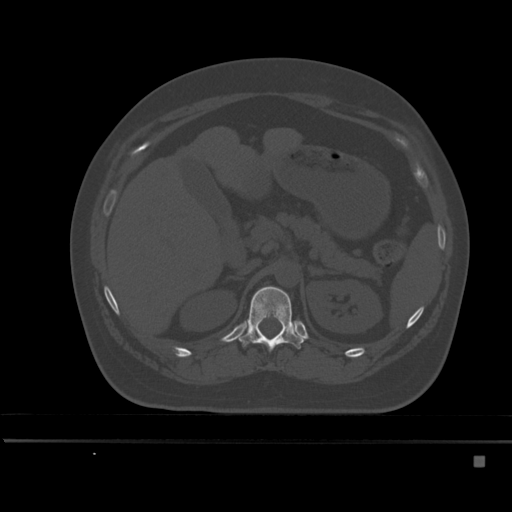
CT including the spine, one axial slice. Position 214 of 495 along the scan axis. Bone window (W 1800 / L 400 HU). 1.5 mm slice thickness. 512 × 512 image matrix, field of view 404 × 404 mm. Female patient, age 33 years. From the clinical record (not read from this slice): primary cancer: breast.
Structures marked on this image (semi-automatically segmented with operator editing):
- T12 vertebra: box from (x=237, y=286) to (x=303, y=350) px